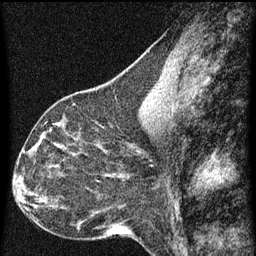
Breast MRI (dynamic contrast-enhanced), one sagittal slice. Position 30 of 60 along the scan axis. Dynamic contrast-enhanced series, image 2 of 3 at this slice position (ordered by acquisition). 1.5 T. TE 4.2 ms, TR 8 ms. 2 mm slice thickness. 256 × 256 image matrix, field of view 180 × 180 mm. Patient: female, 44 years.
Annotated regions visible in this slice (semi-automatically segmented with operator editing):
- analysis volume of interest (the breast-tissue region the enhancement analysis was run in; not a lesion): bounding box [x1, y1, x2, y2] px = [49, 128, 95, 169]
- tumour enhancement mask (voxels above the 70 % enhancement threshold inside the analysis volume of interest): [49, 128, 79, 167]